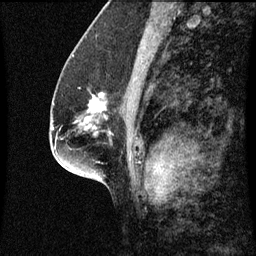
Breast MRI (dynamic contrast-enhanced), one sagittal slice. Slice 31 of 60 in the series (ordered by position). Dynamic contrast-enhanced series, image 2 of 3 at this slice position (ordered by acquisition). 1.5 T. TE 4.2 ms, TR 8.9 ms. 2 mm slice thickness. 256 × 256 image matrix, field of view 200 × 200 mm. Female patient, age 57 years. Case-level facts recorded for this patient, not image findings: setting: breast cancer imaged before/during neoadjuvant chemotherapy; receptor status: HR-positive, HER2-negative.
Outlined on this slice (semi-automatic segmentation, software-assisted and operator-edited):
- analysis volume of interest (the breast-tissue region the enhancement analysis was run in; not a lesion): bounding box (x1, y1, x2, y2) in pixels: (82, 90, 124, 125)
- tumour enhancement mask (voxels above the 70 % enhancement threshold inside the analysis volume of interest): (94, 92, 105, 97)